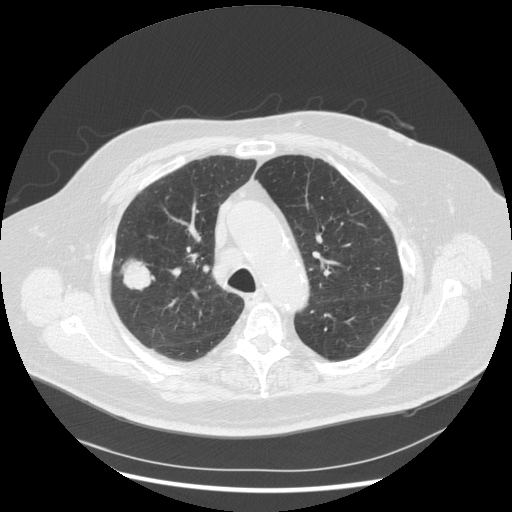
Chest CT (low-dose screening protocol), one axial image. Third screening round (two years after baseline). Lung window (W 1500 / L -600 HU). 2.5 mm slice thickness. 512 × 512 image matrix, field of view 400 × 400 mm. Male participant, aged 72 years at enrolment. Former smoker at enrolment.
Expert-annotated lung lesion, bounding box <108,251,162,300> (left, top, right, bottom; pixels). Screening reader's record for this exam (one nodule recorded; not confirmed to be the boxed lesion): non-calcified nodule or mass ≥4 mm, right upper lobe, 31 × 31 mm, poorly defined margins, soft tissue attenuation, pre-existing on the prior screen: no. Official screen result: positive, other.